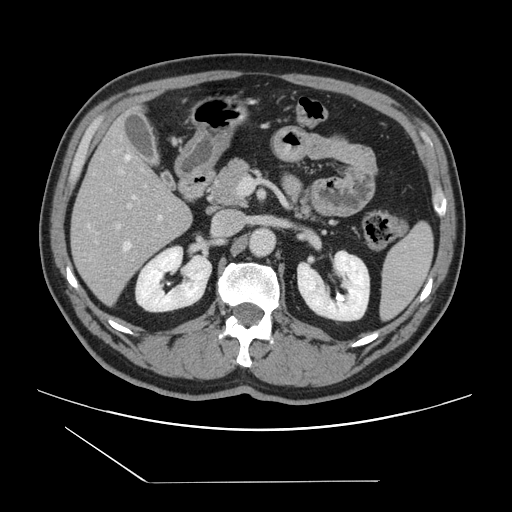
Contrast-enhanced abdominal CT, one axial slice; position 70 of 157 along the scan axis; intravenous contrast given; soft-tissue window (W 400 / L 40 HU); 2.5 mm slice thickness; 512 × 512 image matrix, field of view 407 × 407 mm. Male patient, age 61 years. Case-level facts recorded for this patient, not image findings: diagnosis: colorectal cancer liver metastases, imaged before liver resection; multiple liver metastases: yes; largest metastasis: 5.5 cm.
Outlined on this slice (expert manual segmentation):
- hepatic veins: box from (x=89, y=155) to (x=136, y=250) px
- liver: (x=72, y=126)–(x=192, y=304)
- planned liver remnant (the part of the liver to remain after resection): (x=73, y=125)–(x=179, y=219)
- portal vein (with intrahepatic branches): (x=117, y=169)–(x=162, y=227)